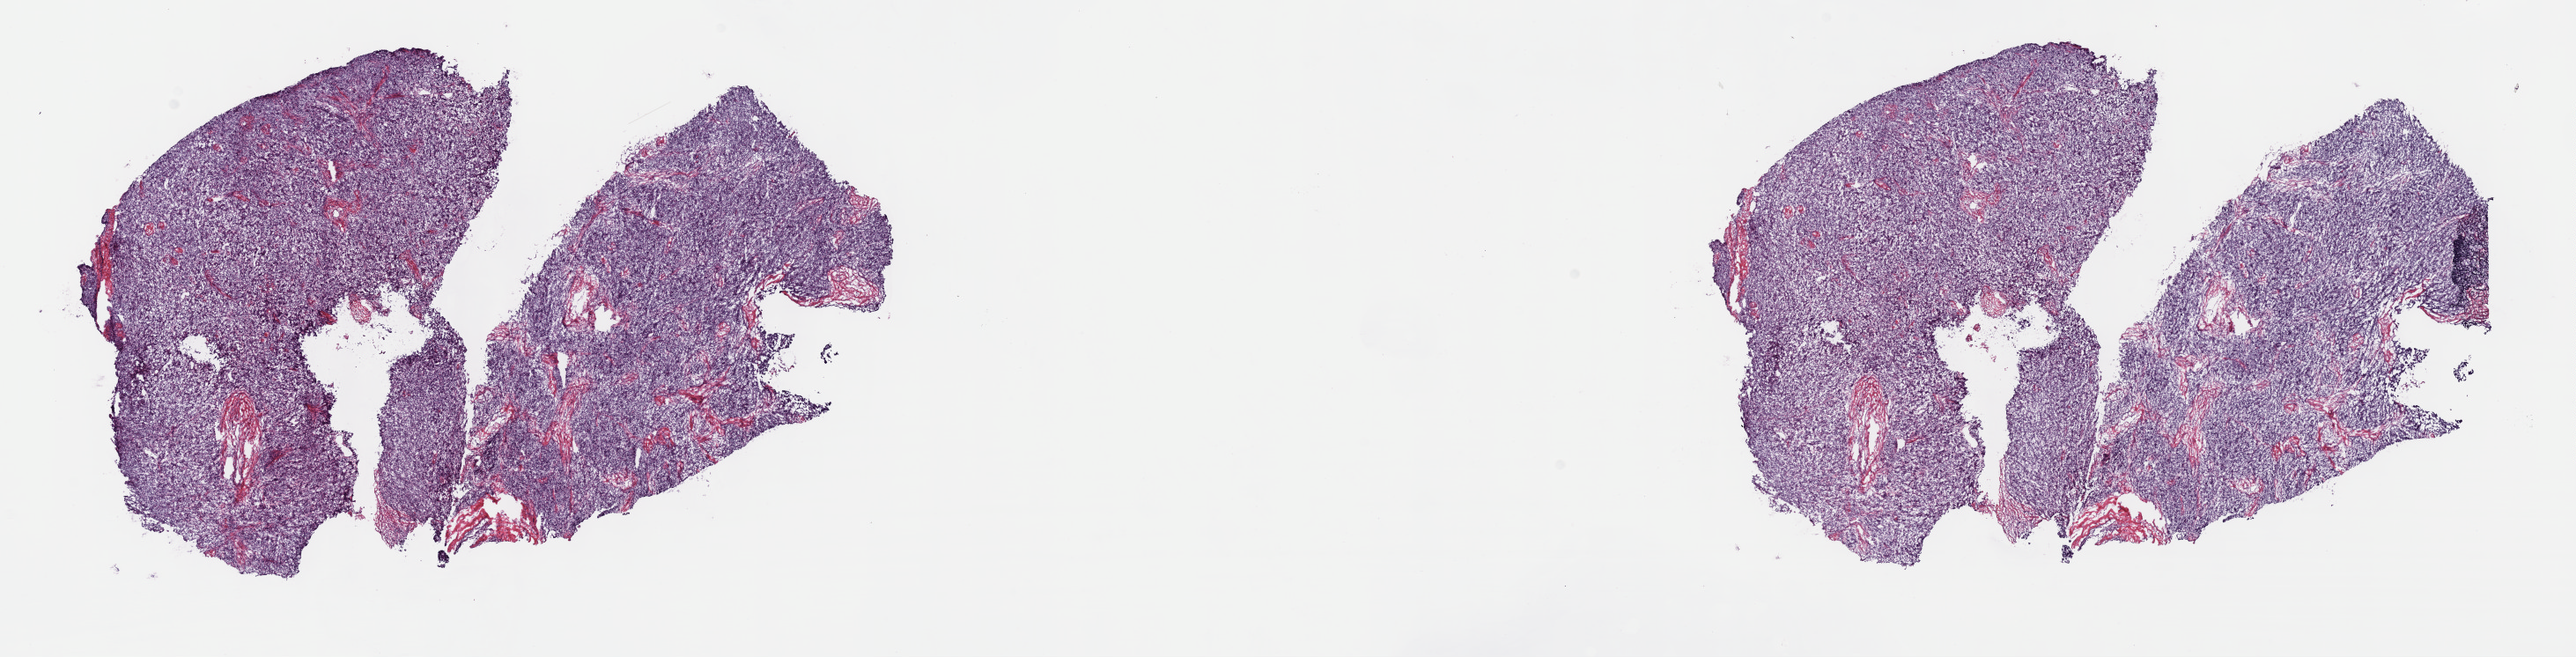
Whole-slide histology image, H&E-stained — low-resolution overview of the scanned area, about 23.7 x 6.0 mm (from a 40x scan), frozen section from the top of the tissue portion, thymus, primary tumour sample. Male, age 66 years at initial diagnosis.
Histologic diagnosis: Thymoma, type A, malignant.